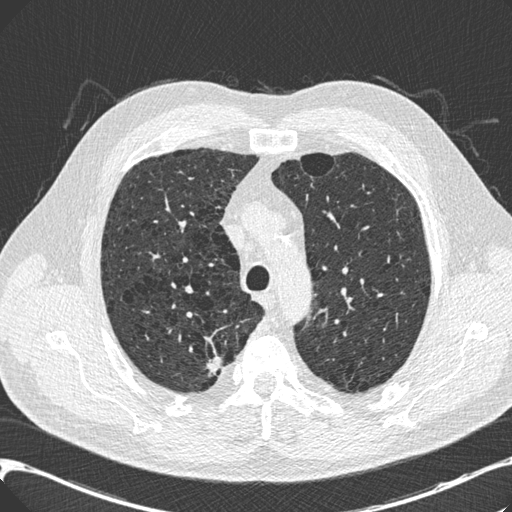
Chest CT (low-dose screening protocol), one axial image. Third screening round (two years after baseline). Lung window (W 1500 / L -600 HU). 0.75 mm slice thickness. Standard (soft-tissue) reconstruction kernel (B30f). 120 kVp. Slice 48 of 197 in the series. 512 × 512 image matrix, field of view 367 × 367 mm. Male participant, aged 68 years at enrolment. Current smoker at enrolment.
Lesion marked by an expert reader, bounding box (x1, y1, x2, y2) in pixels: (189, 347, 235, 388). The screening reader recorded 3 non-calcified nodules or masses ≥4 mm on this exam (right upper lobe, right upper lobe, left lower lobe); which of them this box marks is not recorded. Official screen result: positive, other. Later outcome: lung cancer diagnosed 46 days after this screen — adenocarcinoma, NOS, right upper lobe, well differentiated (G1), stage IB (AJCC 6th edition), 15 mm at pathology.